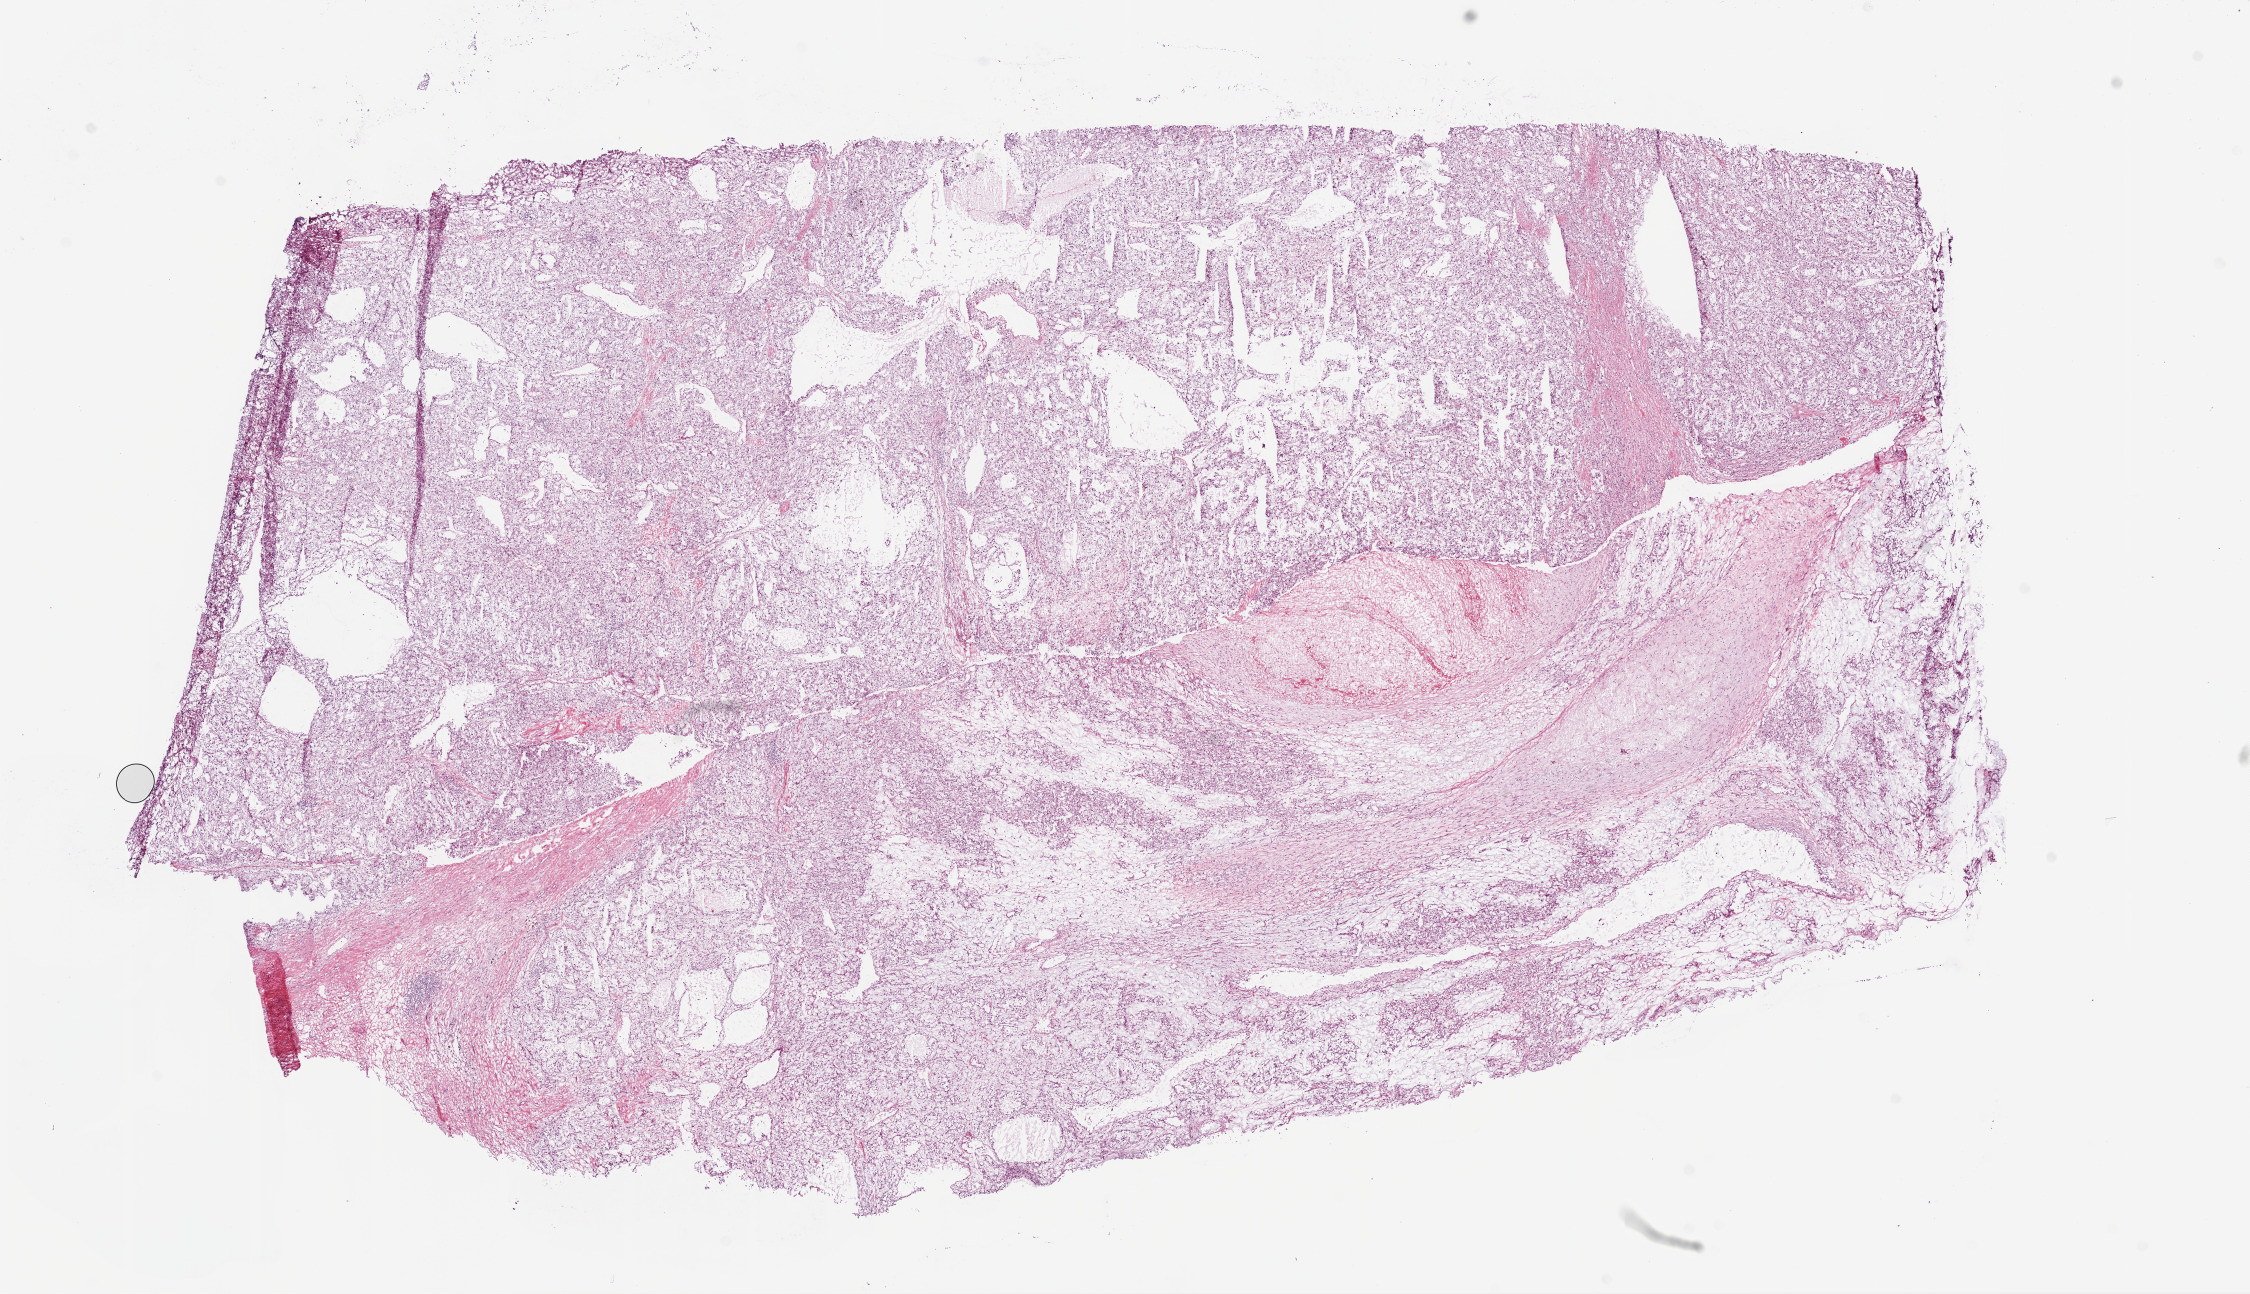
Whole-slide histology image, Hematoxylin and eosin (H&E) stained, shown as a low-resolution overview of the whole scanned area (about 18.1 x 10.4 mm, slide scanned at 20x); frozen section; kidney, primary tumour sample. Patient: male, age at initial diagnosis 81 years. Histologic grade: G3 (poorly differentiated). Composition of this section per pathologist review: tumour cells 80%, tumour nuclei 85%, normal cells 0%, stromal cells 20%, necrosis 0%.
AJCC pathologic stage: III. Laterality: right. Histologic diagnosis: Clear cell adenocarcinoma, NOS.